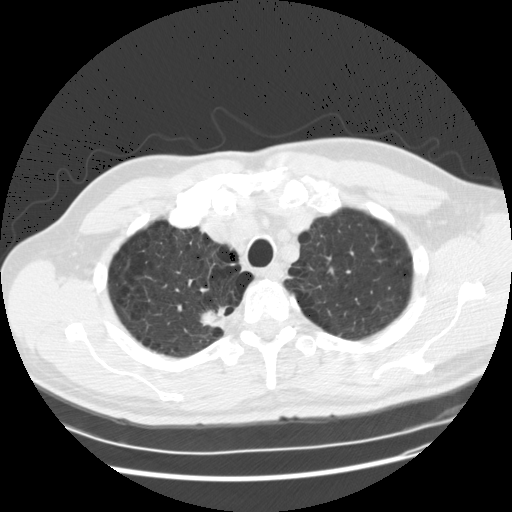
Chest CT (low-dose screening protocol), one axial image; baseline annual screen; lung window (W 1500 / L -600 HU); 2.5 mm slice thickness; standard (soft-tissue) reconstruction kernel (STANDARD); slice 23 of 132 in the series. Male, age 61 years at enrolment.
• Expert reader's lesion annotation, bounding box (x1, y1, x2, y2) in pixels: (195, 291, 235, 341).
• Reader record for this screening exam (exam-level; its link to the box is not recorded): non-calcified nodule or mass ≥4 mm, right upper lobe, 19 × 13 mm, poorly defined margins, soft tissue attenuation.
• Official screen result: positive, change unspecified: nodule(s) >= 4 mm or enlarging nodule(s), mass(es), or other non-specific abnormalities suspicious for lung cancer.
• Later outcome: lung cancer diagnosed 62 days after this screen — squamous cell carcinoma, NOS, right upper lobe, poorly differentiated (G3), stage IA (AJCC 6th edition), 20 mm at pathology.